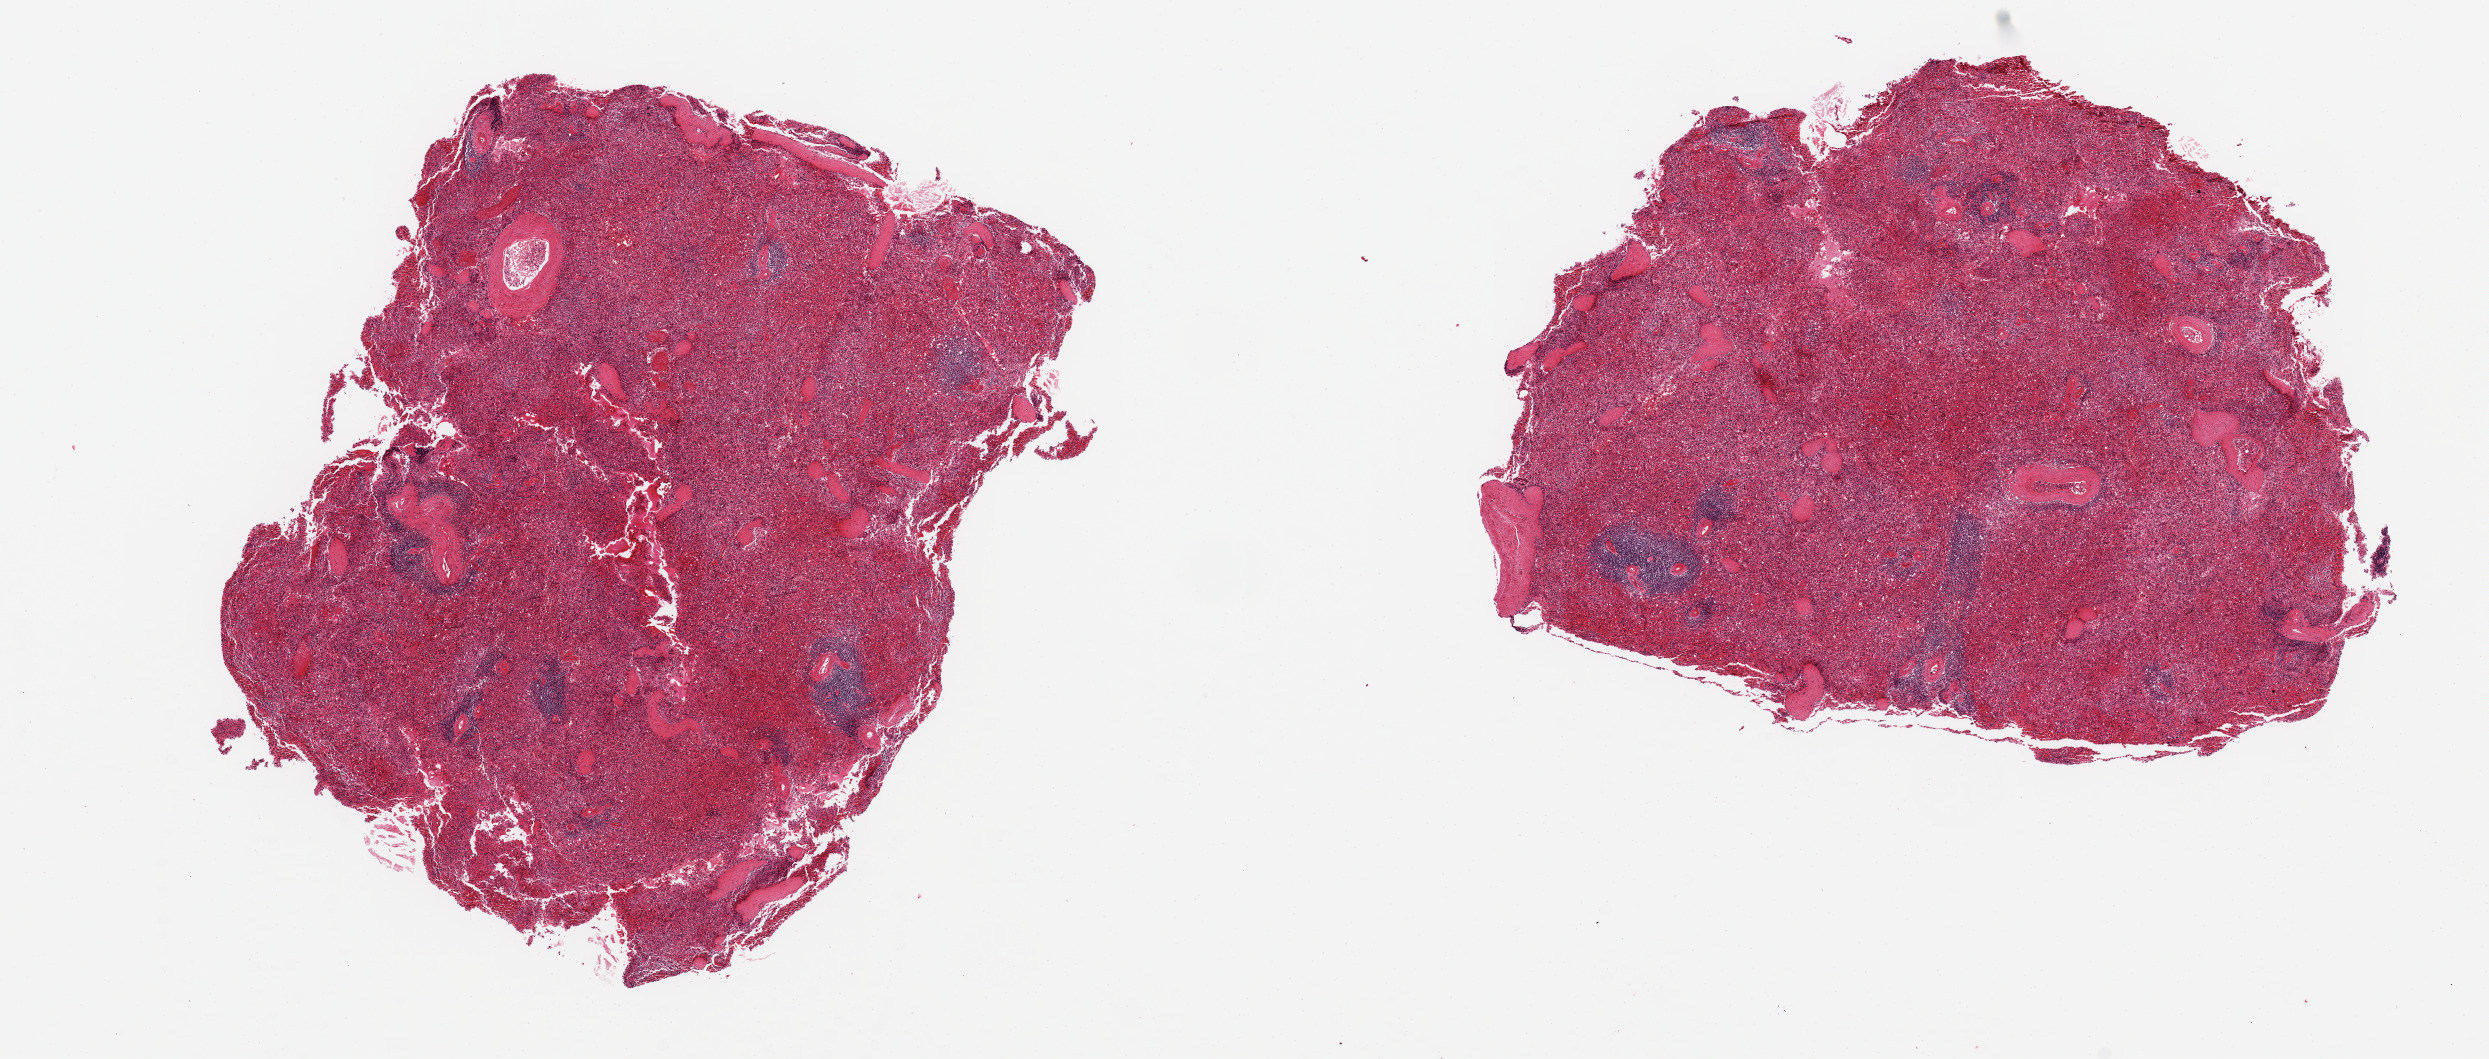
Digitized hematoxylin and eosin (H&E)-stained section, whole scanned area (about 19.7 x 8.4 mm, slide scanned at 20x) shown as a low-resolution overview; PAXgene-fixed, paraffin-embedded tissue; sampled site (target tissue): spleen; tissue donor sample. Donor sex: male.
- reviewer comment on this tissue sample: 2 aliquots, ~6.5x5mm. Poorly processed & badly autolyzed